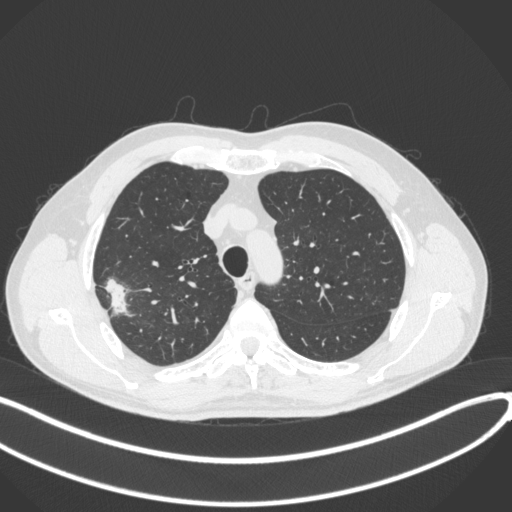
Chest CT, one axial slice; slice 322 of 381 in the series (ordered by position); reconstruction kernel B31f; lung window (W 1500 / L -600 HU); 1 mm slice thickness; 512 × 512 image matrix, field of view 400 × 400 mm. Male patient, age 62 years. From the clinical record (not read from this slice): clinical TNM (as recorded): T1c N0 M0; histopathological grade: G2-3.
Outlined on this slice (bounding box drawn by a radiologist):
- lung tumour (recorded histology: adenocarcinoma): box from (x=99, y=272) to (x=137, y=318) px